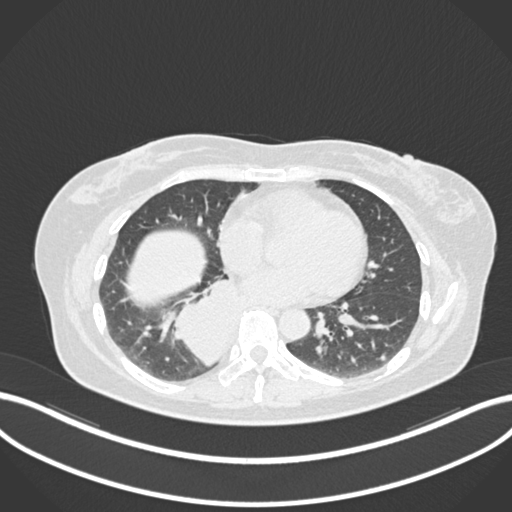
Chest CT, one axial slice; position 564 of 677 along the scan axis; reconstruction kernel B30f; lung window (W 1500 / L -600 HU); 1 mm slice thickness; 512 × 512 image matrix, field of view 400 × 400 mm. Patient: female, 54 years. Case-level facts recorded for this patient, not image findings: clinical TNM (as recorded): T4 N0 M0.
Outlined on this slice (bounding box drawn by a radiologist):
- lung tumour (recorded histology: adenocarcinoma): bounding box <162,276,243,368> (left, top, right, bottom; pixels)